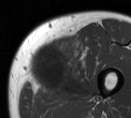
MRI of an extremity soft-tissue mass, one axial slice. Position 18 of 55 along the scan axis. MR volume resampled by the dataset authors to the PET/CT grid (not the native acquisition matrix). 3.27 mm slice thickness. 131 × 118 image matrix. Male patient. Case-level facts recorded for this patient, not image findings: histological type: pleiomorphic liposarcoma; grade: high; site of the primary tumour: left thigh.
Outlined on this slice (expert contour drawn on MRI and transferred to this co-registered scan by the dataset authors):
- gross tumour volume including surrounding oedema: bounding box (x1, y1, x2, y2) in pixels: (27, 39, 94, 101)
- gross tumour volume (mass): (27, 39, 72, 92)